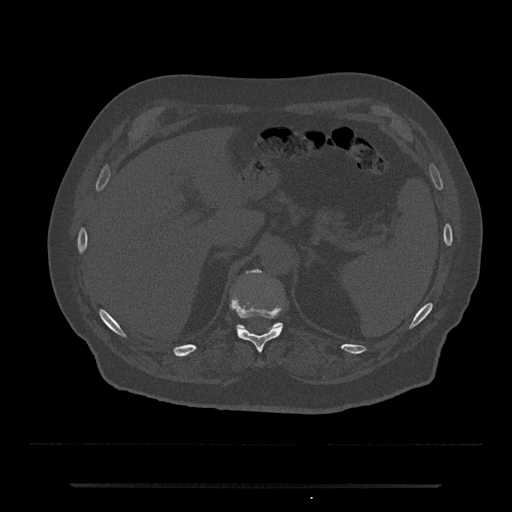
CT including the spine, one axial slice; slice 637 of 797 in the series (ordered by position); reconstruction kernel Br40s/3; 120 kVp; bone window (W 1800 / L 400 HU); 512 × 512 image matrix, field of view 434 × 434 mm. Patient: male, 80 years. From the clinical record (not read from this slice): primary cancer: prostate; vertebrae with lytic lesions (as recorded): L1, T11.
Structures marked on this image (semi-automatically segmented with operator editing):
- T11 vertebra: bounding box (x1, y1, x2, y2) in pixels: (231, 298, 283, 353)
- T12 vertebra: (236, 269, 283, 331)